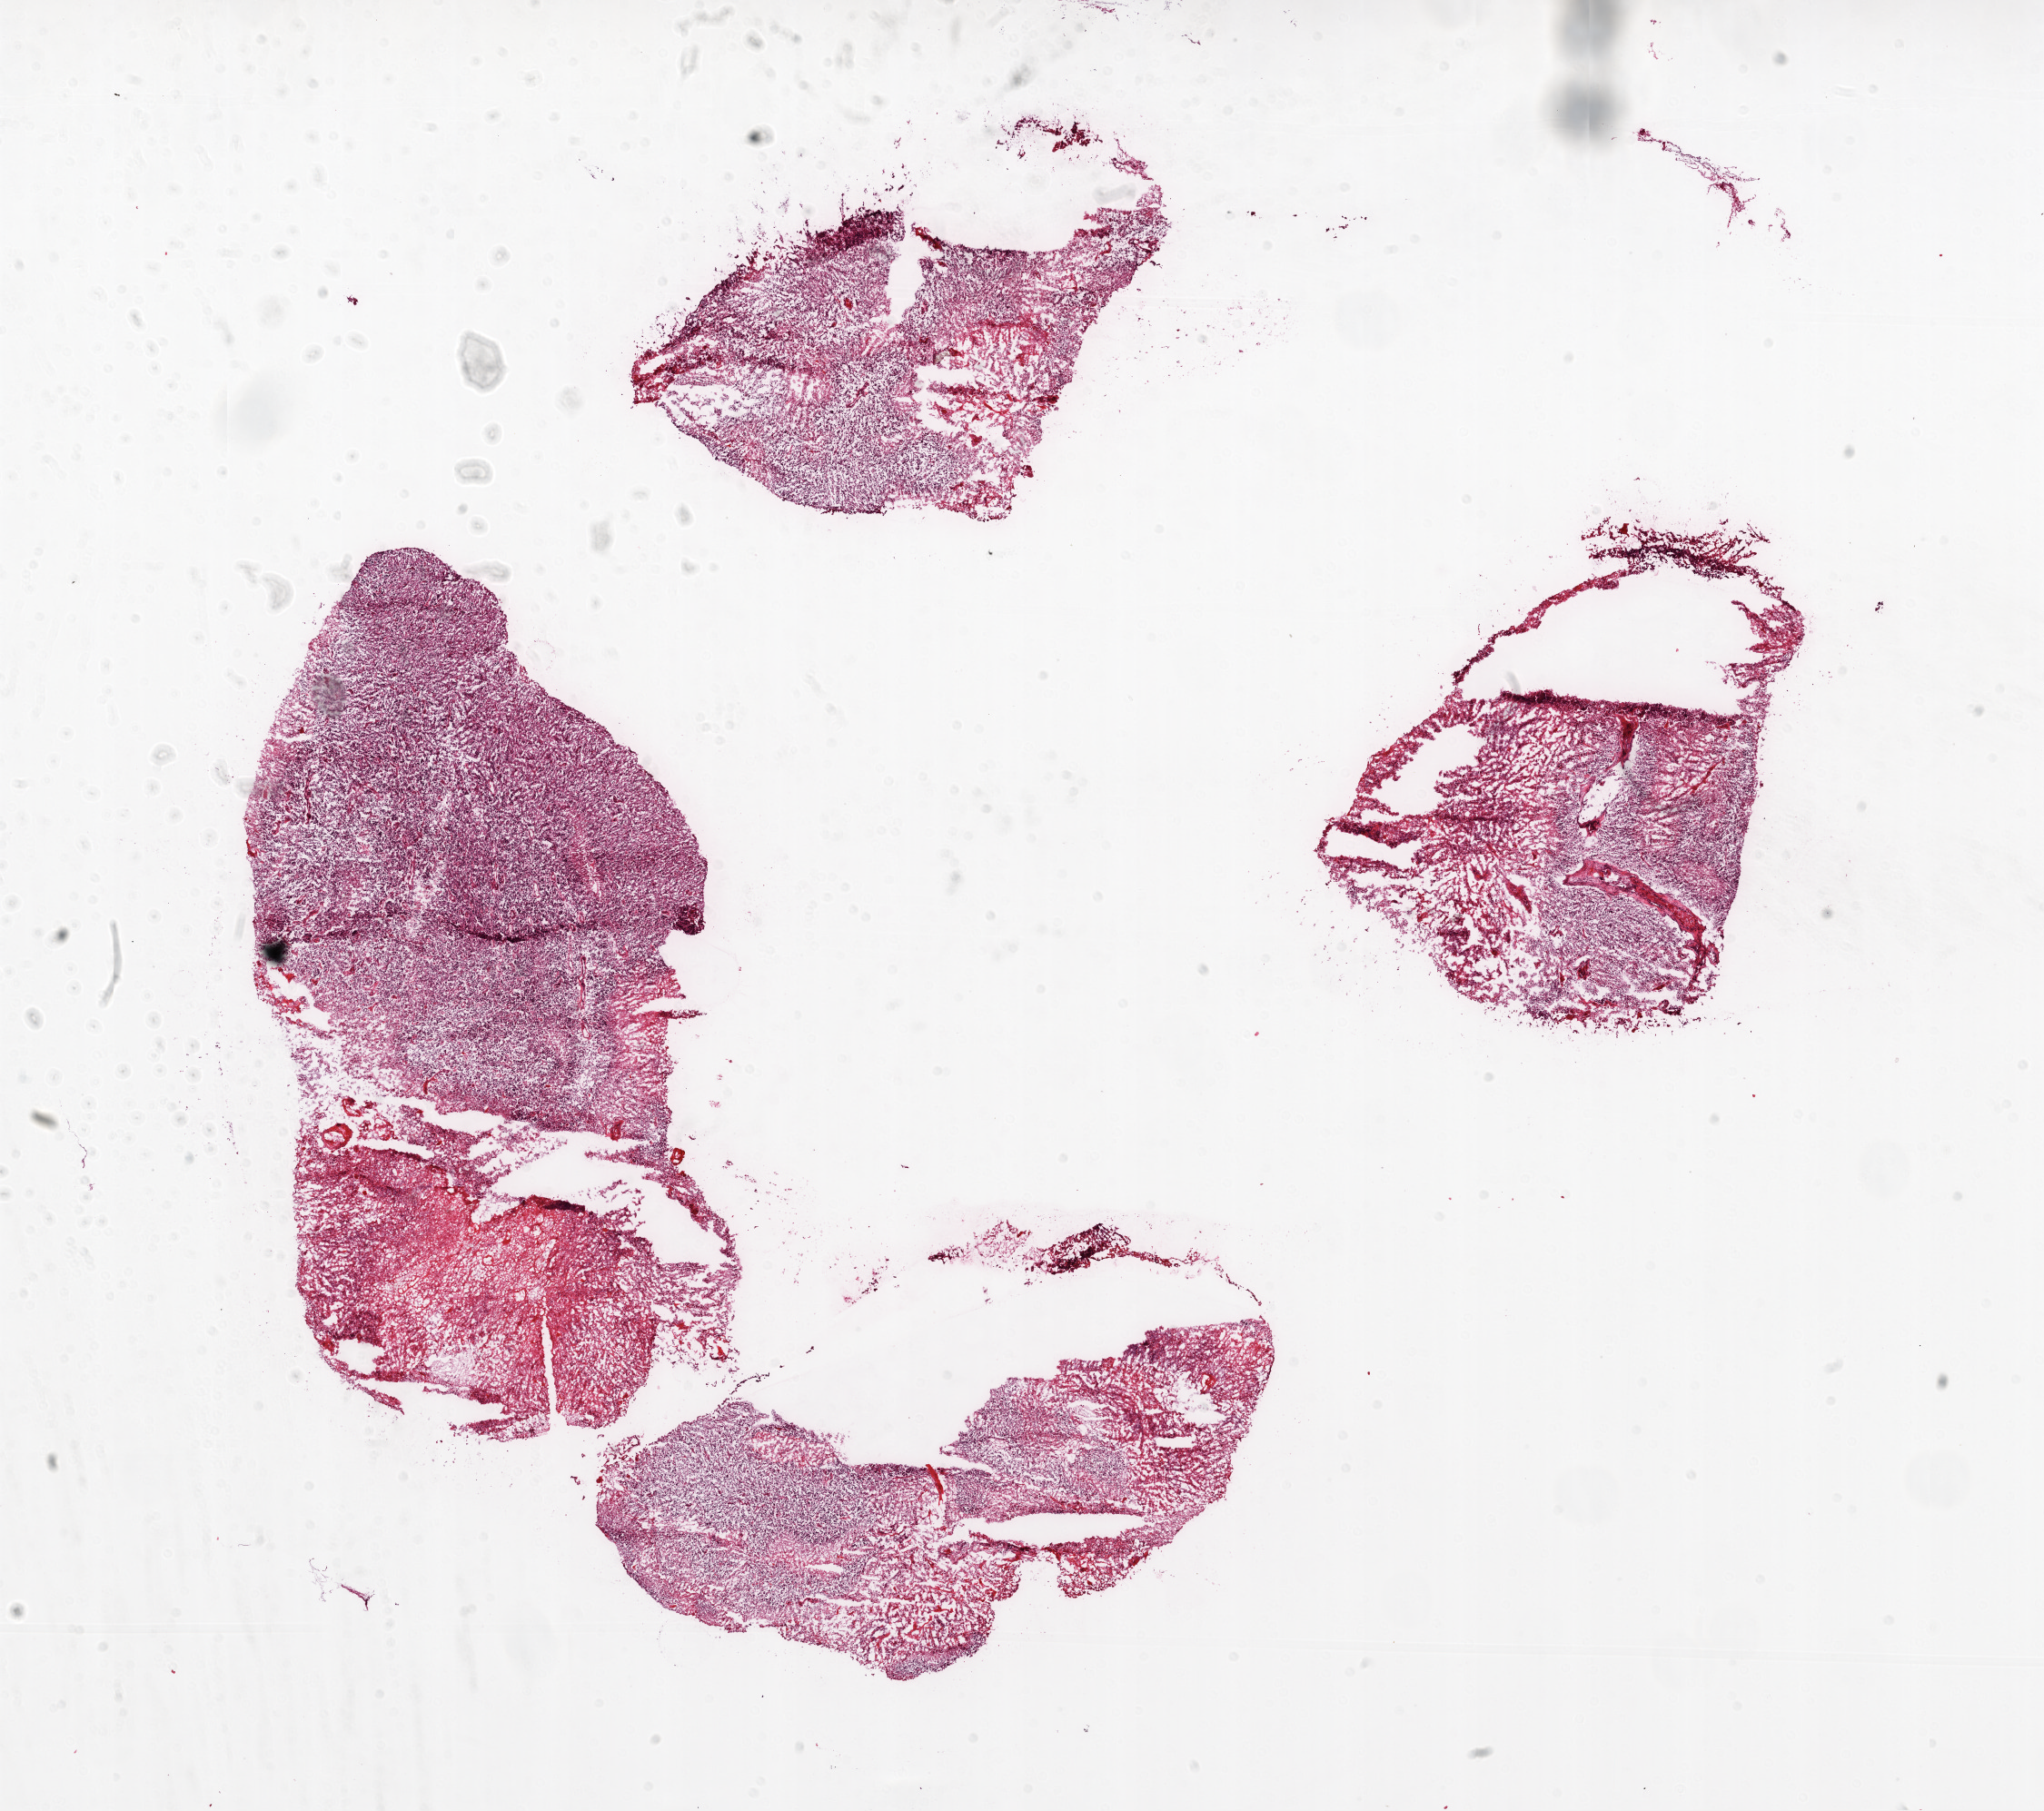
Whole-slide histology image, H&E-stained — whole scanned area (about 18.1 x 16.0 mm, slide scanned at 20x) shown as a low-resolution overview, frozen section from the top of the tissue portion, primary tumour sample from the brain. Male, age 66 years at initial diagnosis. Slide review estimates, as recorded: tumour cells 80%, tumour nuclei 100%.
Pathologic diagnosis: Glioblastoma.